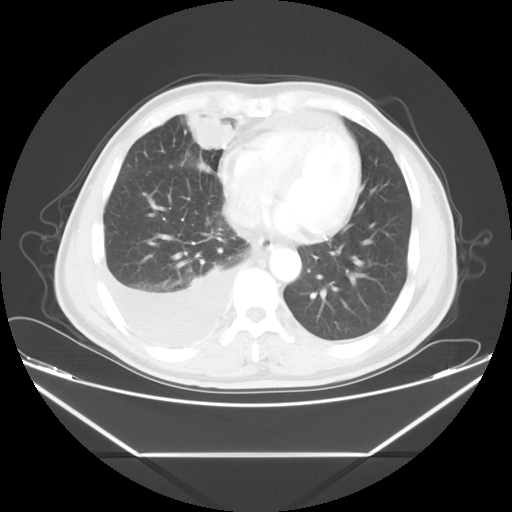
Chest CT, one axial slice. Slice 18 of 56 in the series (ordered by position). Reconstruction kernel STANDARD. 120 kVp. Lung window (W 1500 / L -600 HU). 512 × 512 image matrix, field of view 412 × 412 mm. Male patient, age 57 years. Case-level facts recorded for this patient, not image findings: clinical TNM (as recorded): T2 N3 M1.
Outlined on this slice (bounding box drawn by a radiologist):
- lung tumour (recorded histology: adenocarcinoma): bounding box (x1, y1, x2, y2) in pixels: (187, 112, 239, 151)